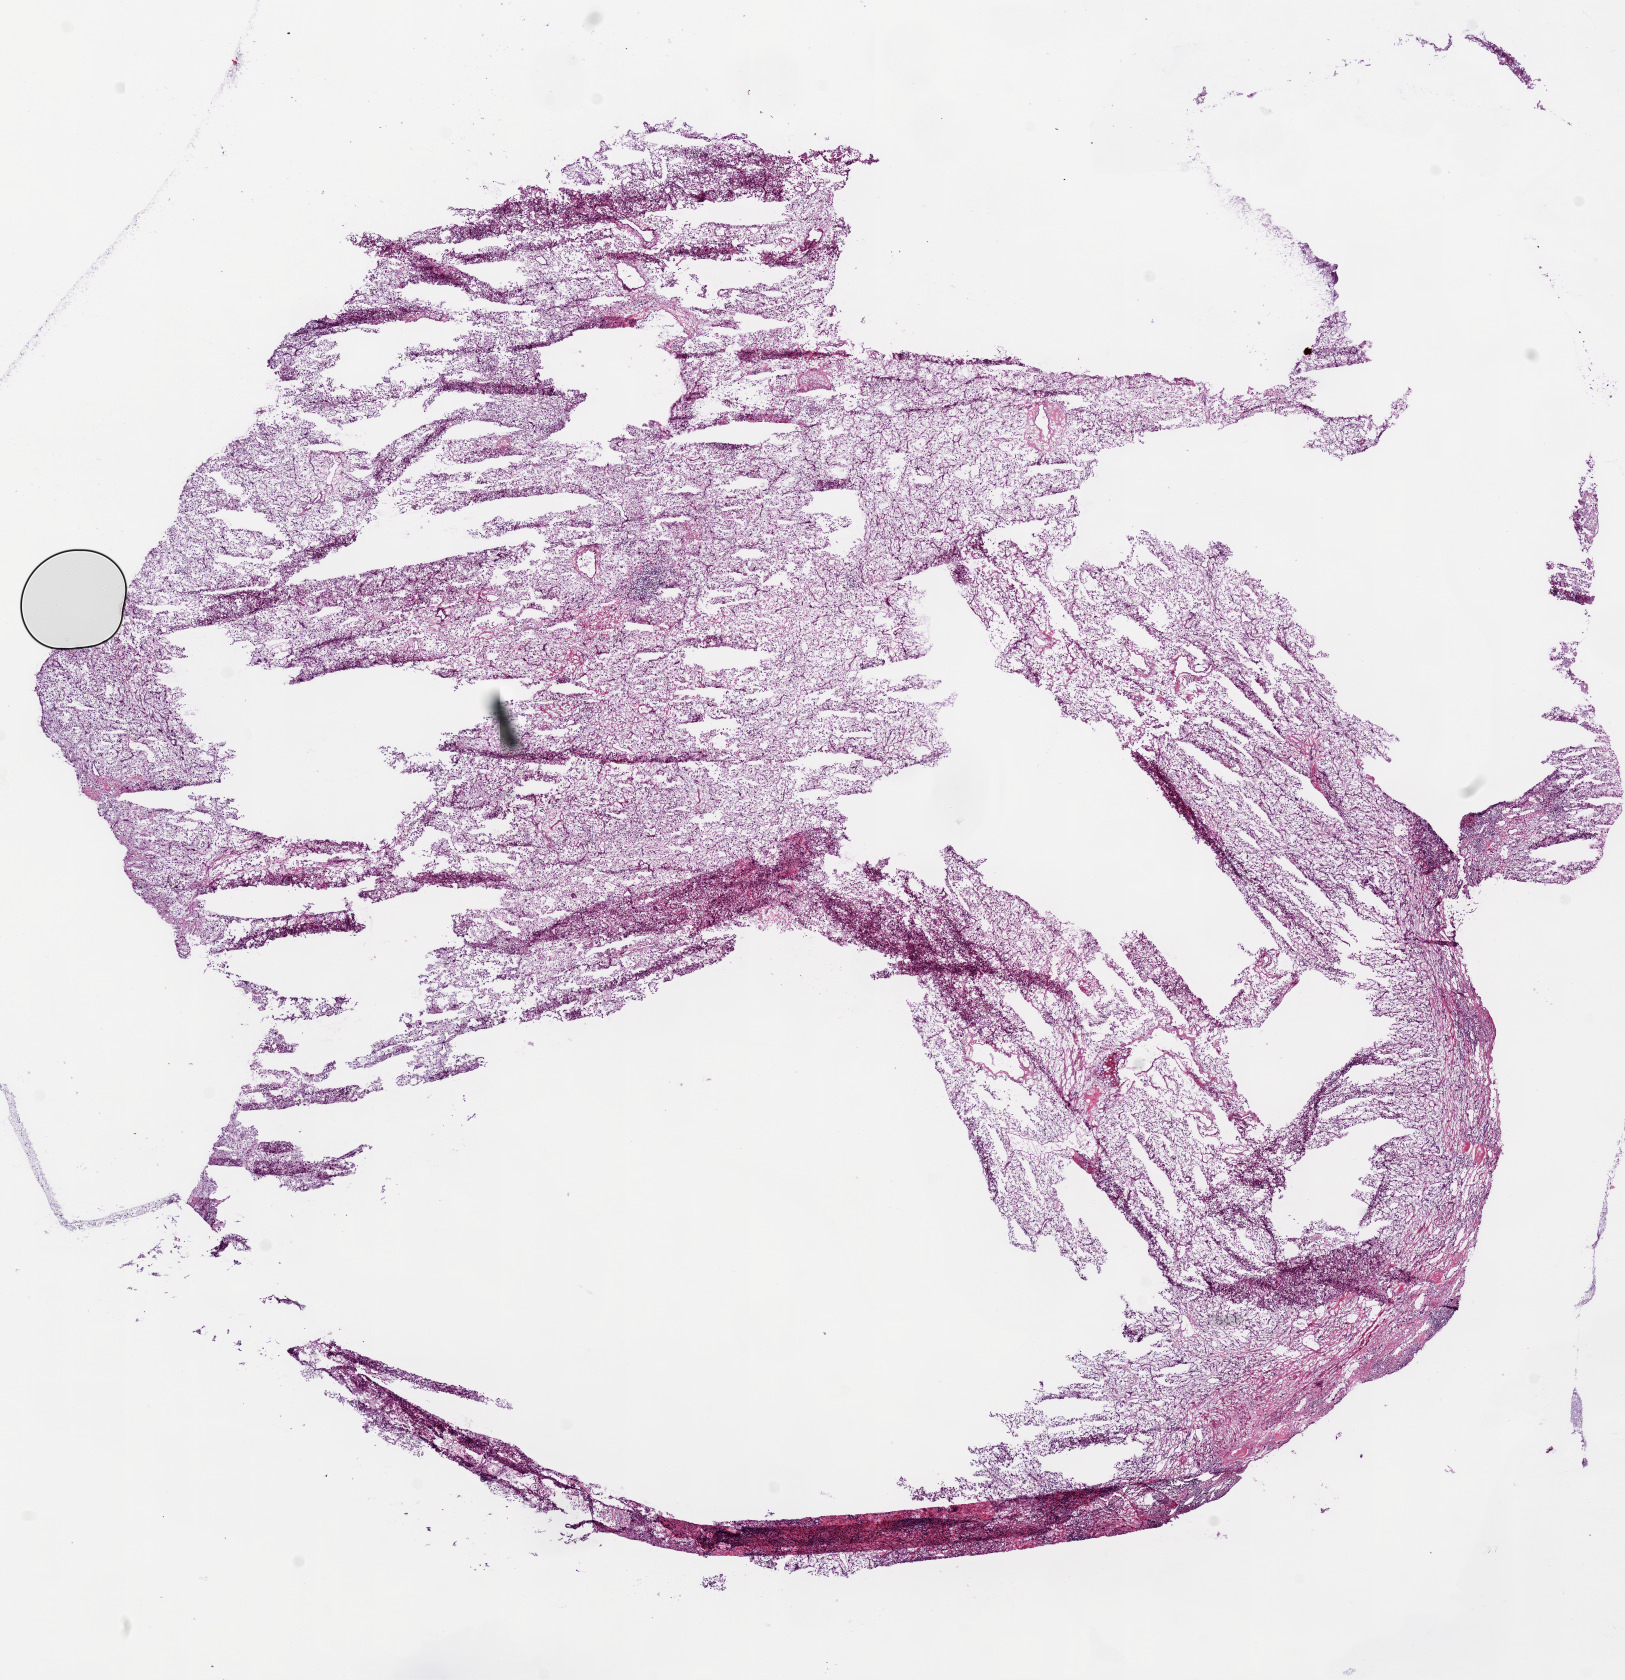
Whole-slide histology image, H&E — shown as a low-resolution overview of the whole scanned area (about 13.0 x 13.5 mm); frozen section; kidney, primary tumour sample. Patient: male, age at initial diagnosis 64 years. Histologic grade: G3 (poorly differentiated). Composition of this section per pathologist review: tumour cells 90%, tumour nuclei 80%, normal cells 0%, stromal cells 10%, necrosis 0%.
• laterality: right
• AJCC pathologic stage: III
• diagnosis: Clear cell adenocarcinoma, NOS
• lymph nodes positive (case pathology): 0 of 7 examined